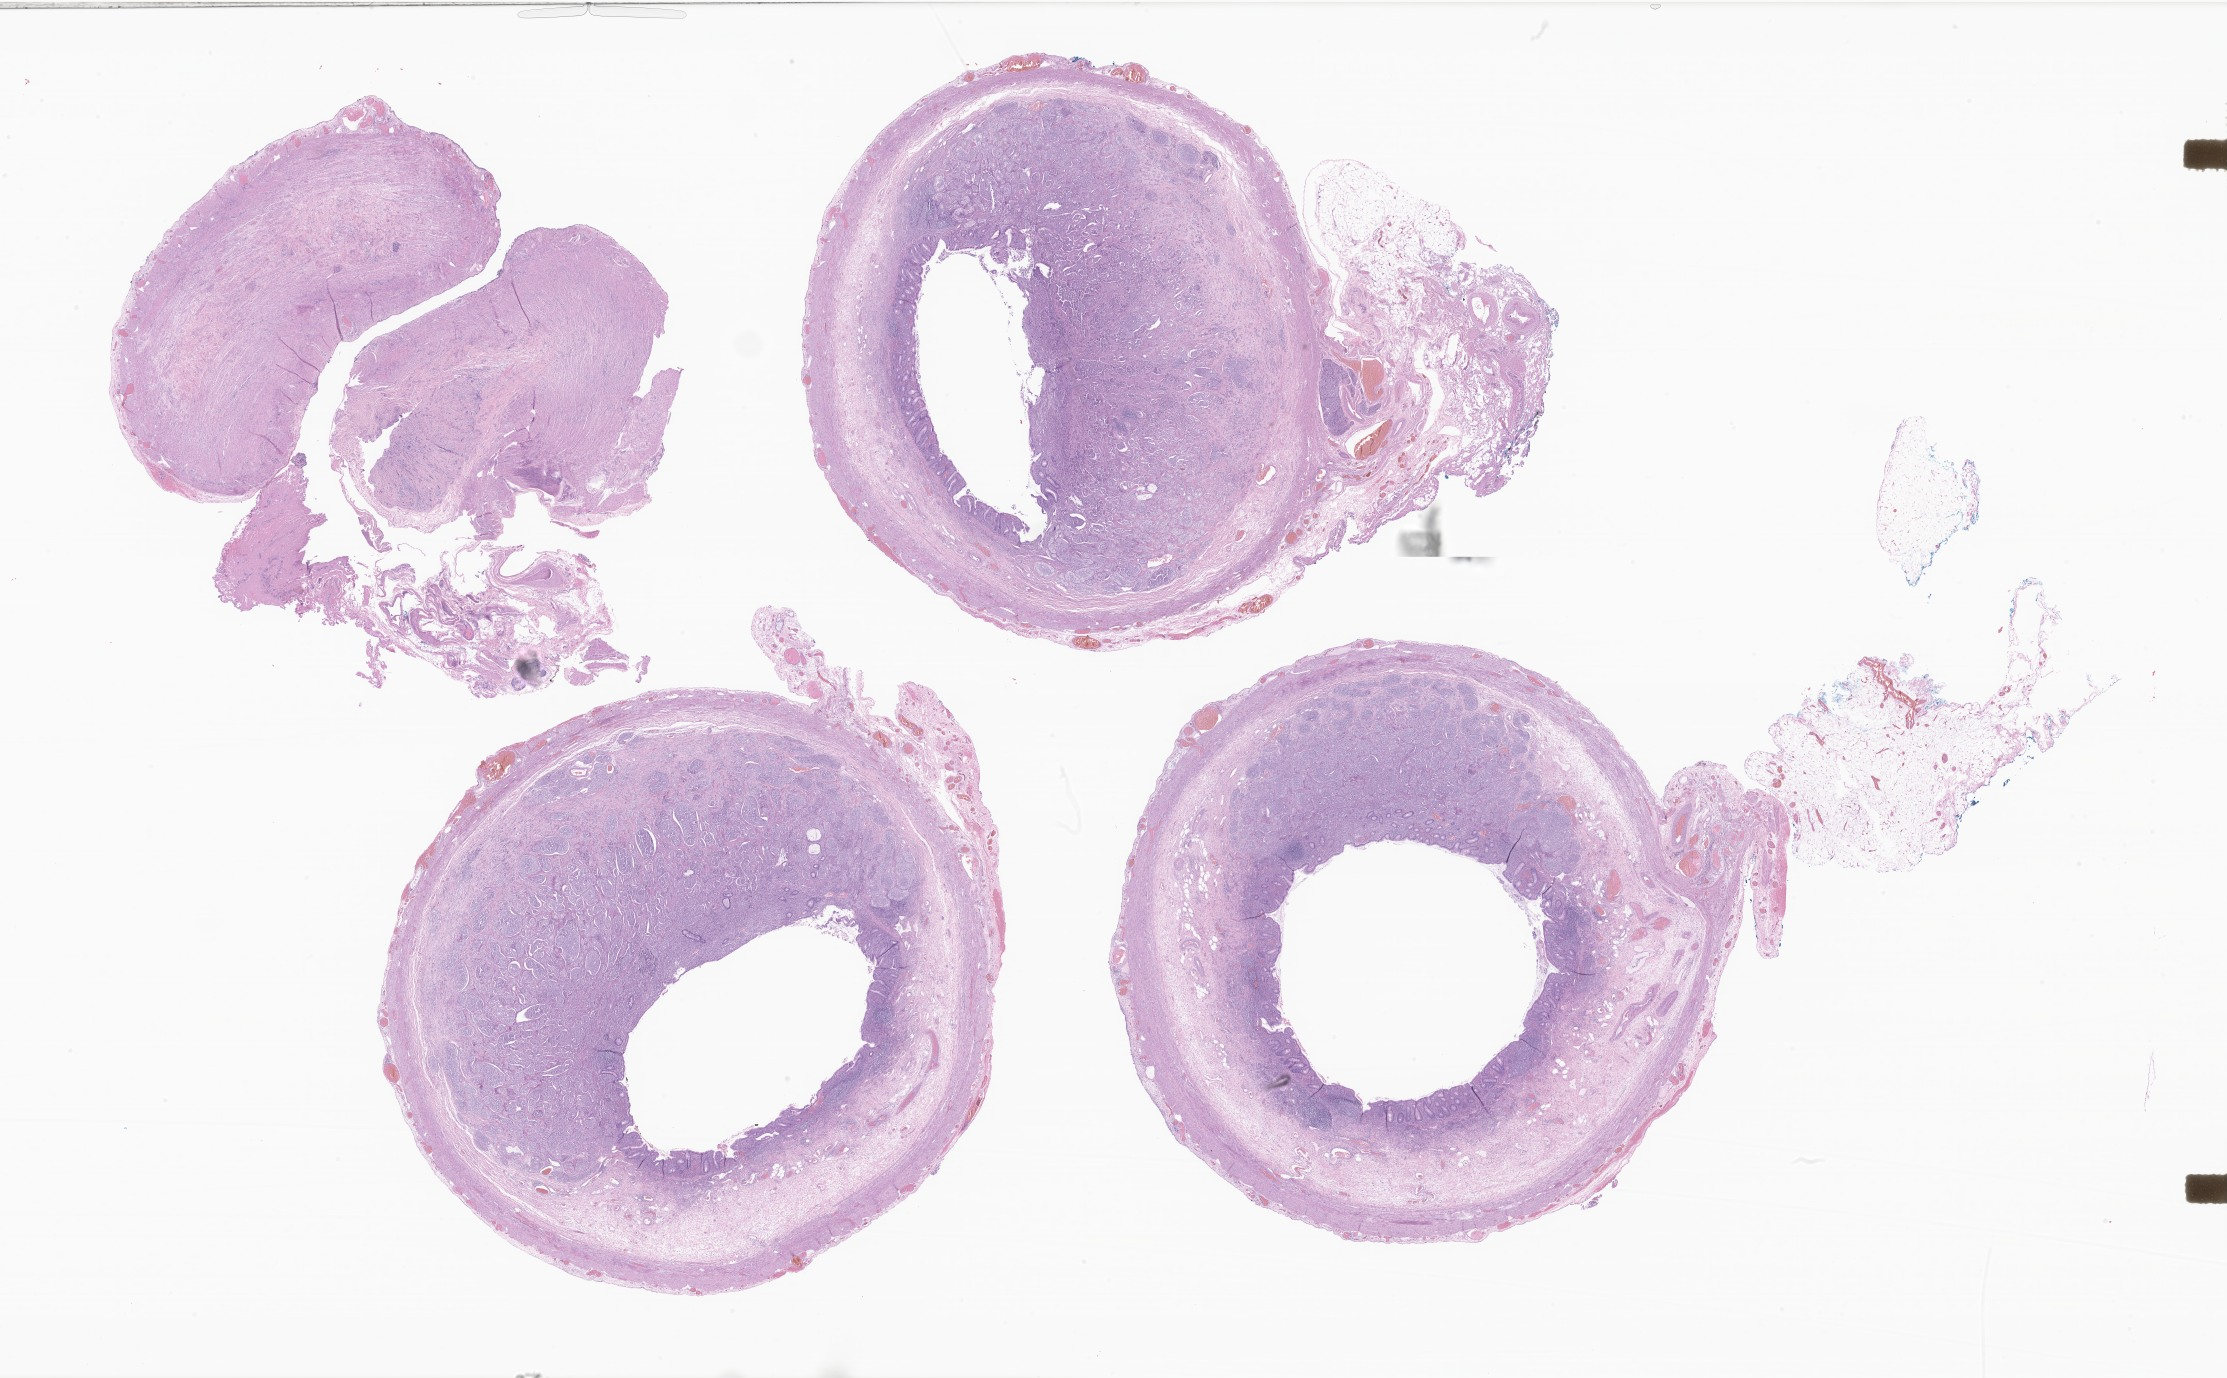
H&E whole-slide image of tumor tissue from the appendix — a low-resolution overview of the entire scanned area, about 37.6 x 23.2 mm; formalin-fixed paraffin-embedded section. Patient: female, age 212 months (17 years 8 months).
* recorded diagnosis: Neuroendocrine carcinoma, NOS